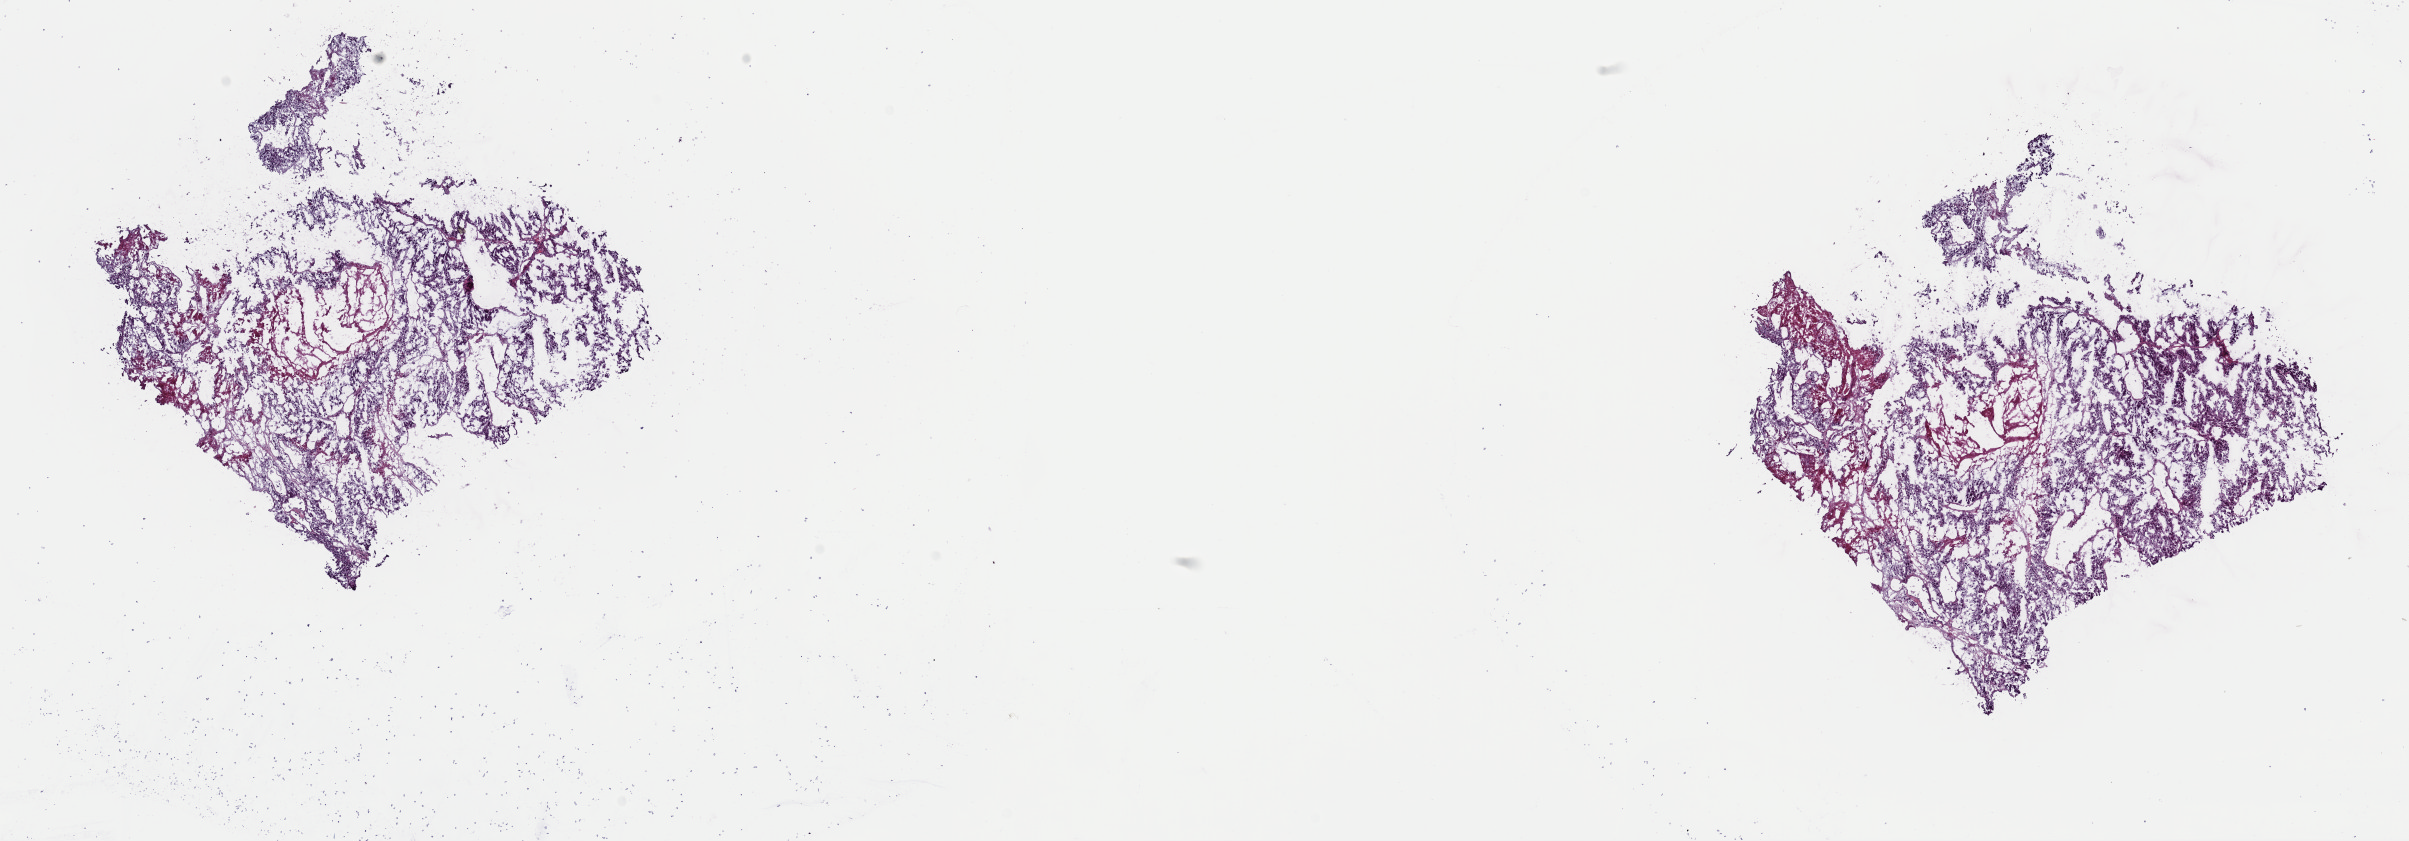
Digitized H&E tissue section (whole slide), shown as a low-resolution overview of the whole scanned area (about 19.0 x 6.6 mm, slide scanned at 40x), frozen section, sample: primary tumour, adrenal cortex. Patient: female, age at initial diagnosis 37 years.
Histologic diagnosis: Adrenal cortical carcinoma (cortex of adrenal gland).